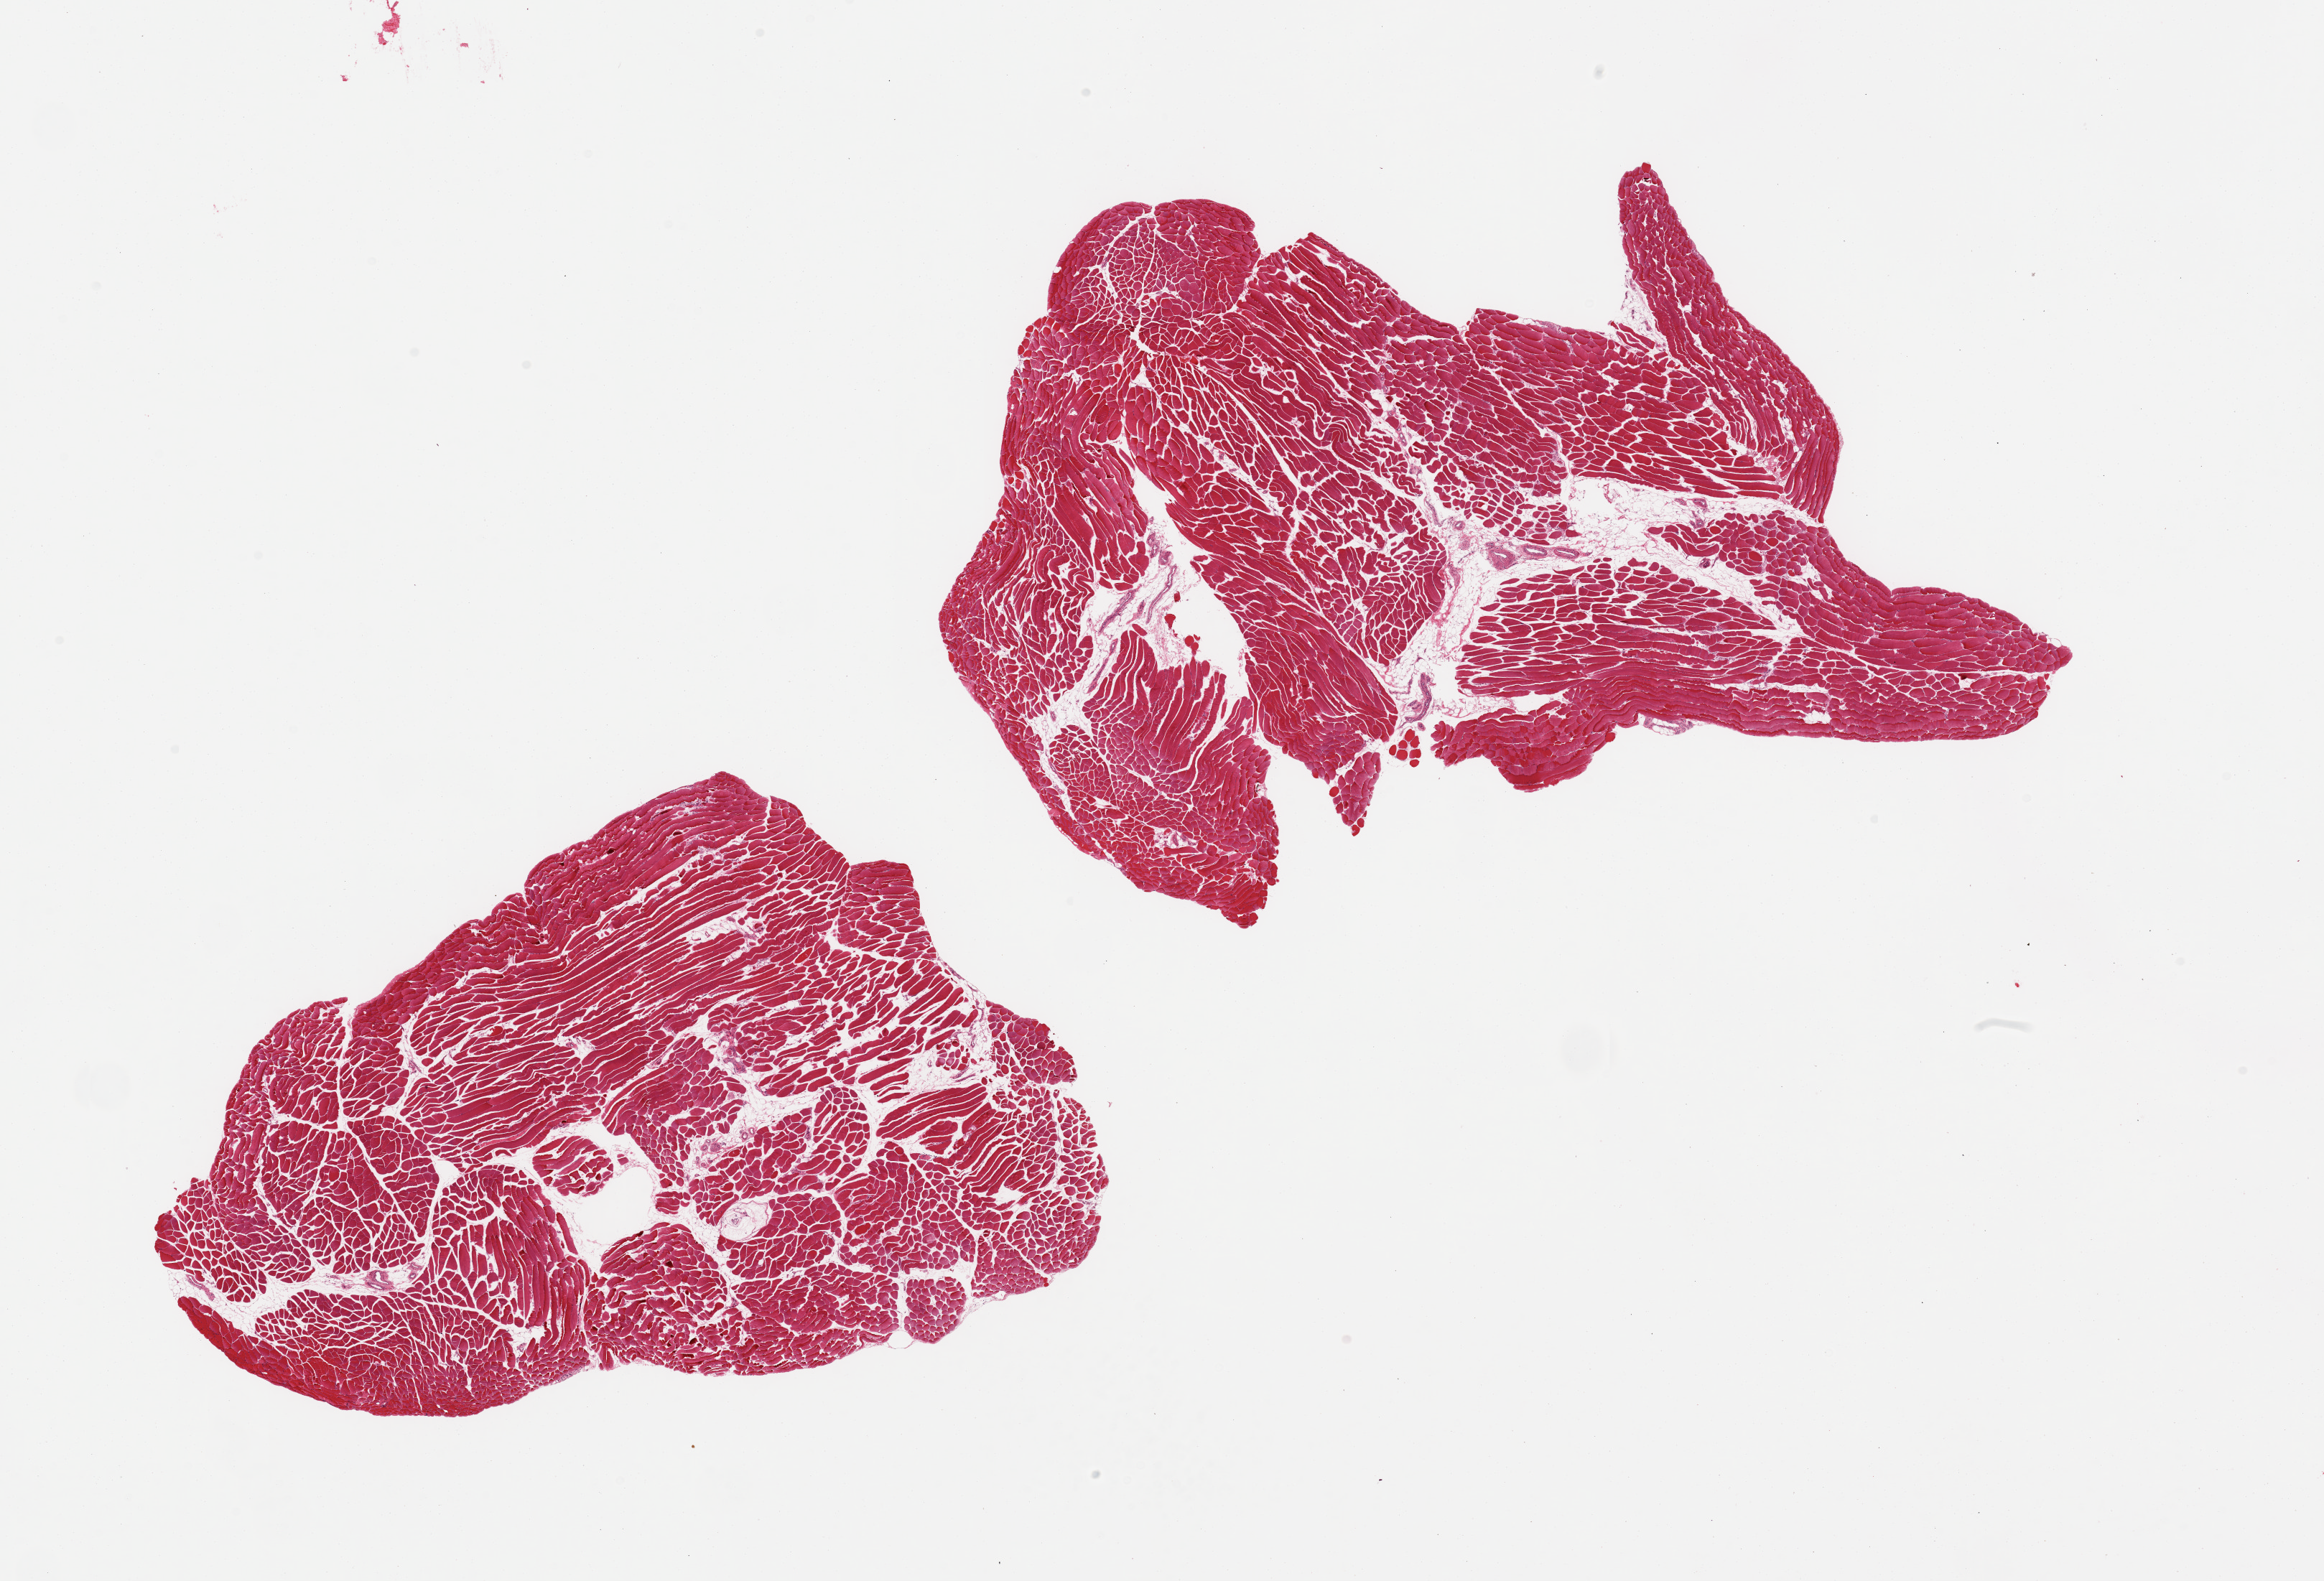
Digitized haematoxylin and eosin-stained section — shown as a low-resolution overview of the whole scanned area (about 25.6 x 17.4 mm, acquisition: 20x scan), PAXgene-fixed paraffin-embedded (PFPE) section, sampled site (target tissue): skeletal muscle, tissue donor sample.
* review note (as recorded): 2 pieces, ~5-10% interstitial fat